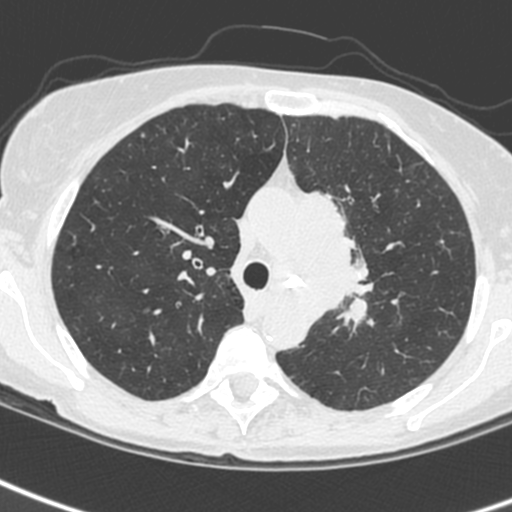
Low-dose screening chest CT, one axial slice; position 174 of 242 along the scan axis; 120 kVp; lung window (W 1500 / L -600 HU); 1.3 mm slice thickness; 512 × 512 image matrix.
Structures marked on this image (outlined manually by an expert reader):
- lesion 3 (tumor, upper lobe of left lung): bounding box (x1, y1, x2, y2) in pixels: (302, 191, 358, 320)